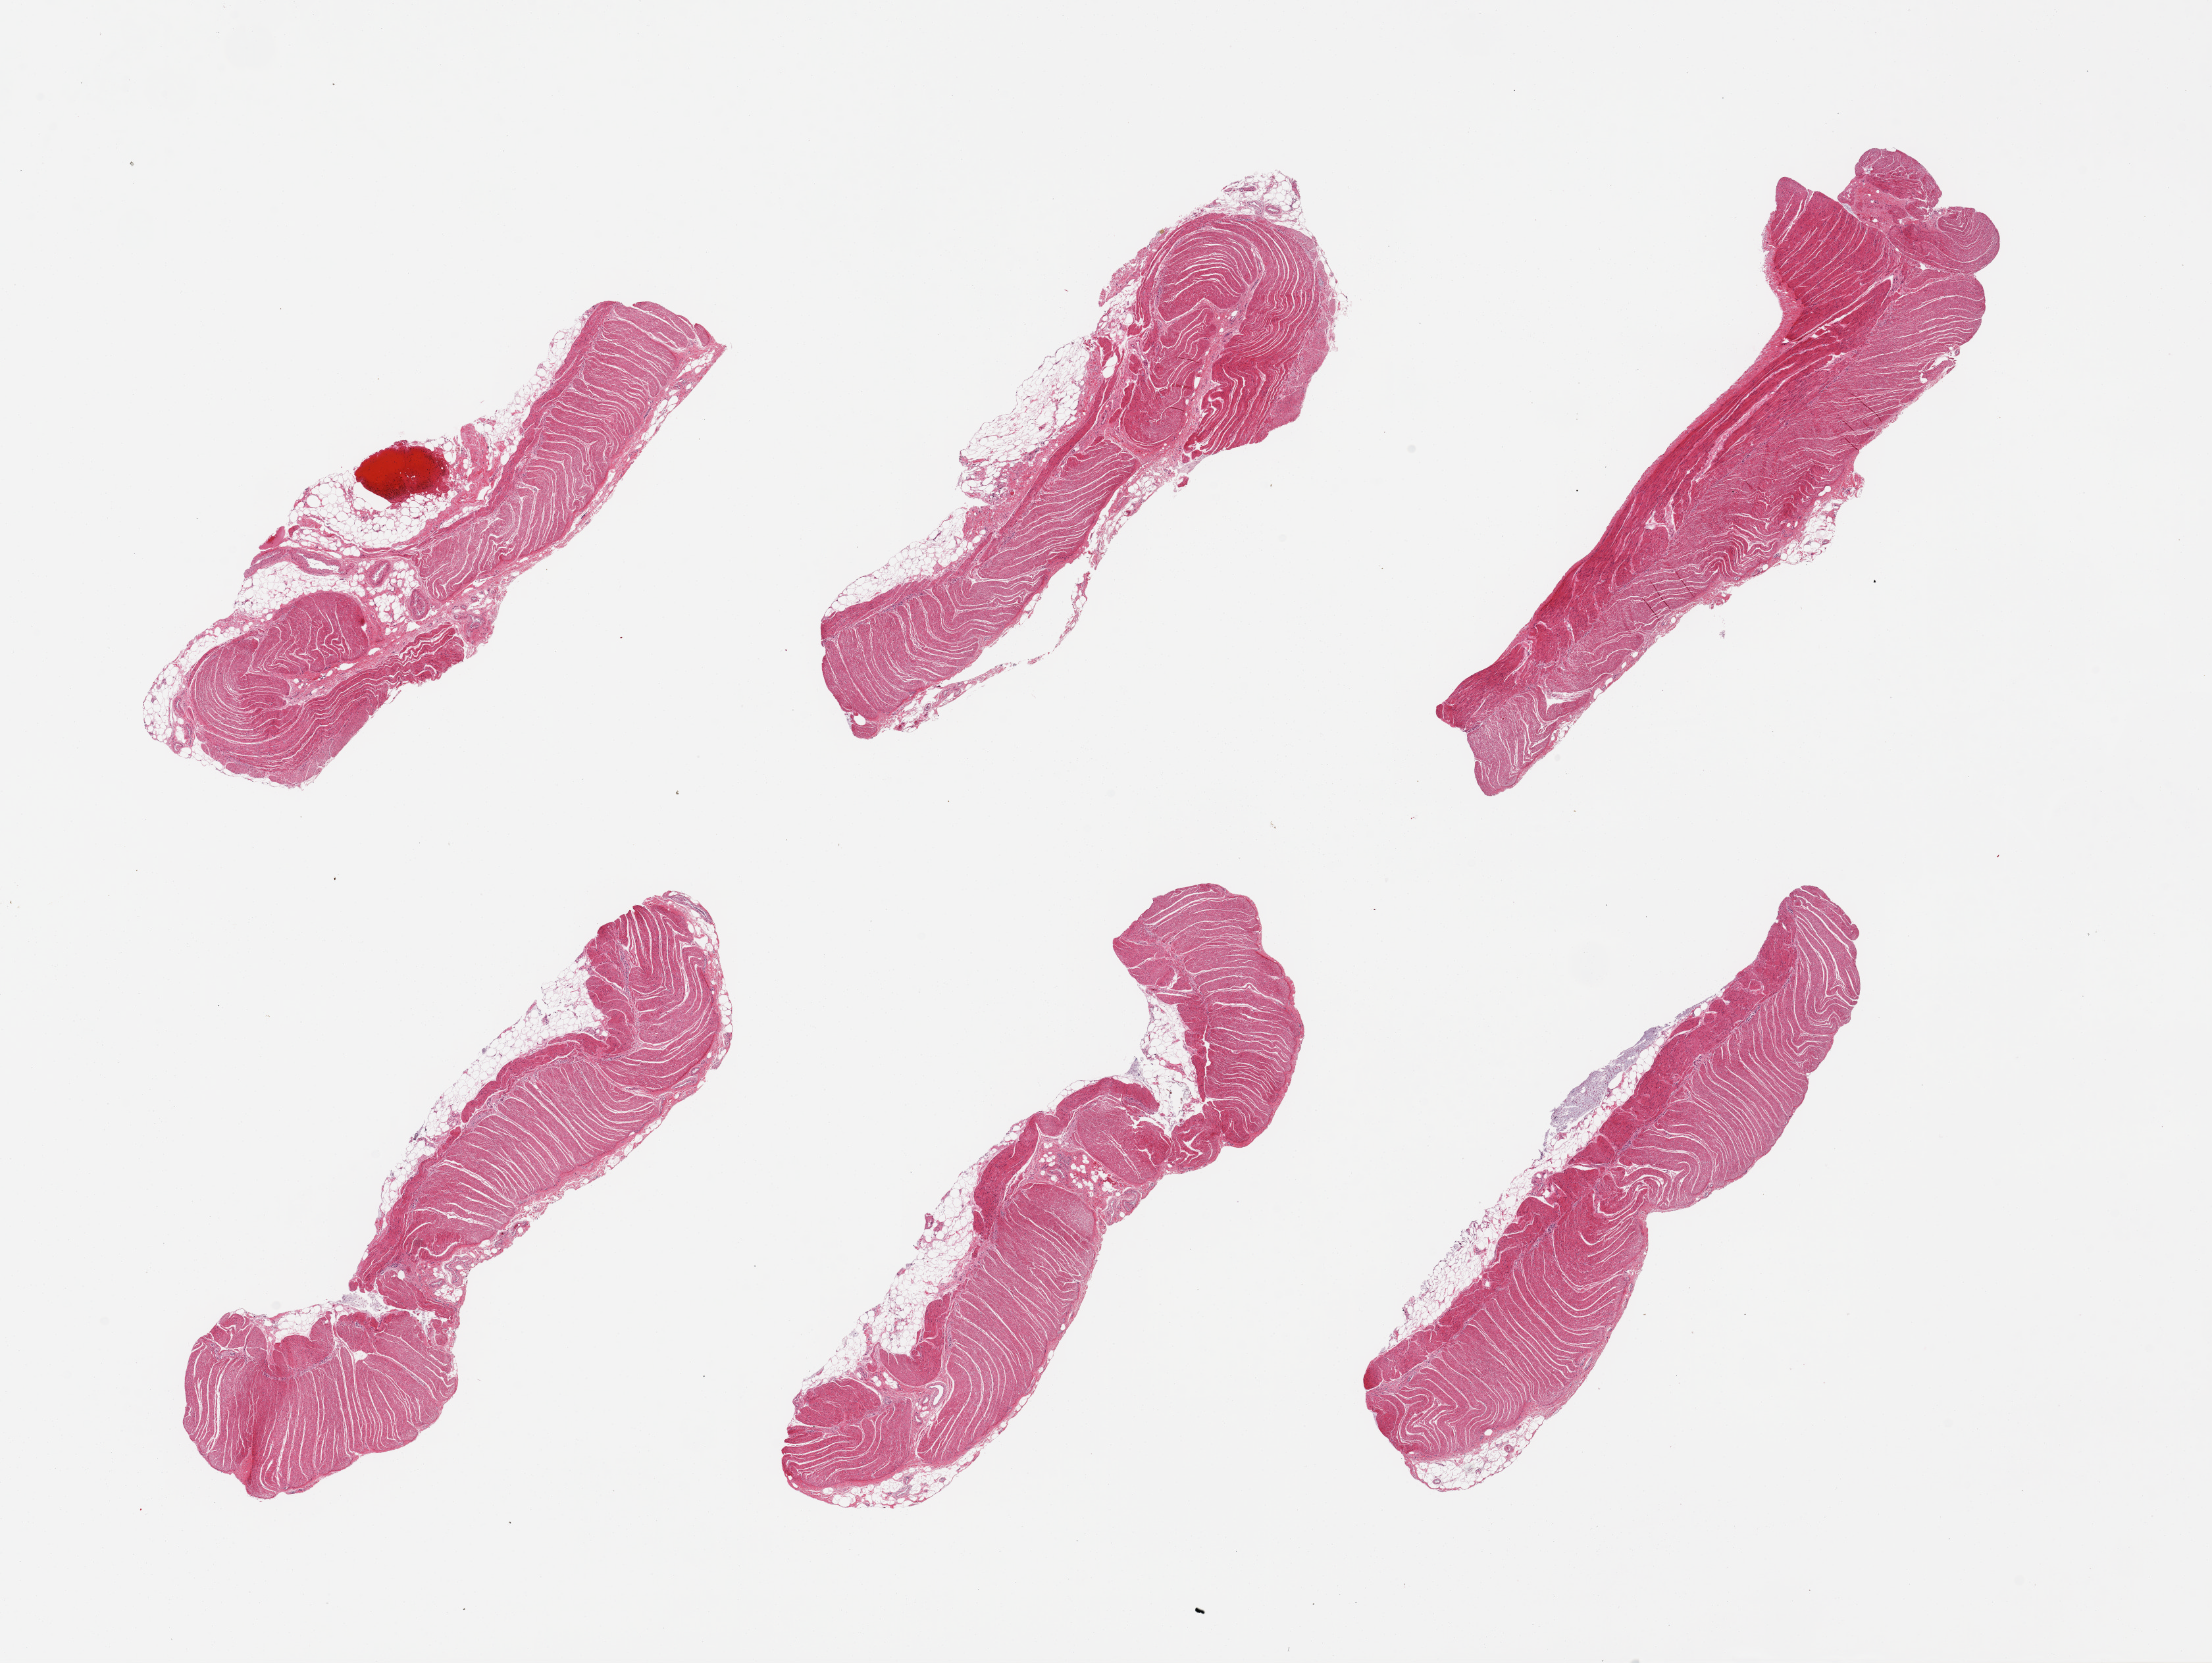
Digitized H&E-stained section, shown as a low-resolution overview of the whole scanned area (about 26.6 x 20.0 mm). PAXgene-fixed paraffin-embedded (PFPE) section. Target tissue: sigmoid colon. Donor tissue sample. Donor: male.
- pathologist's review note for this sample: 6 pieces; colonic type muscularis propria with 10% external fat